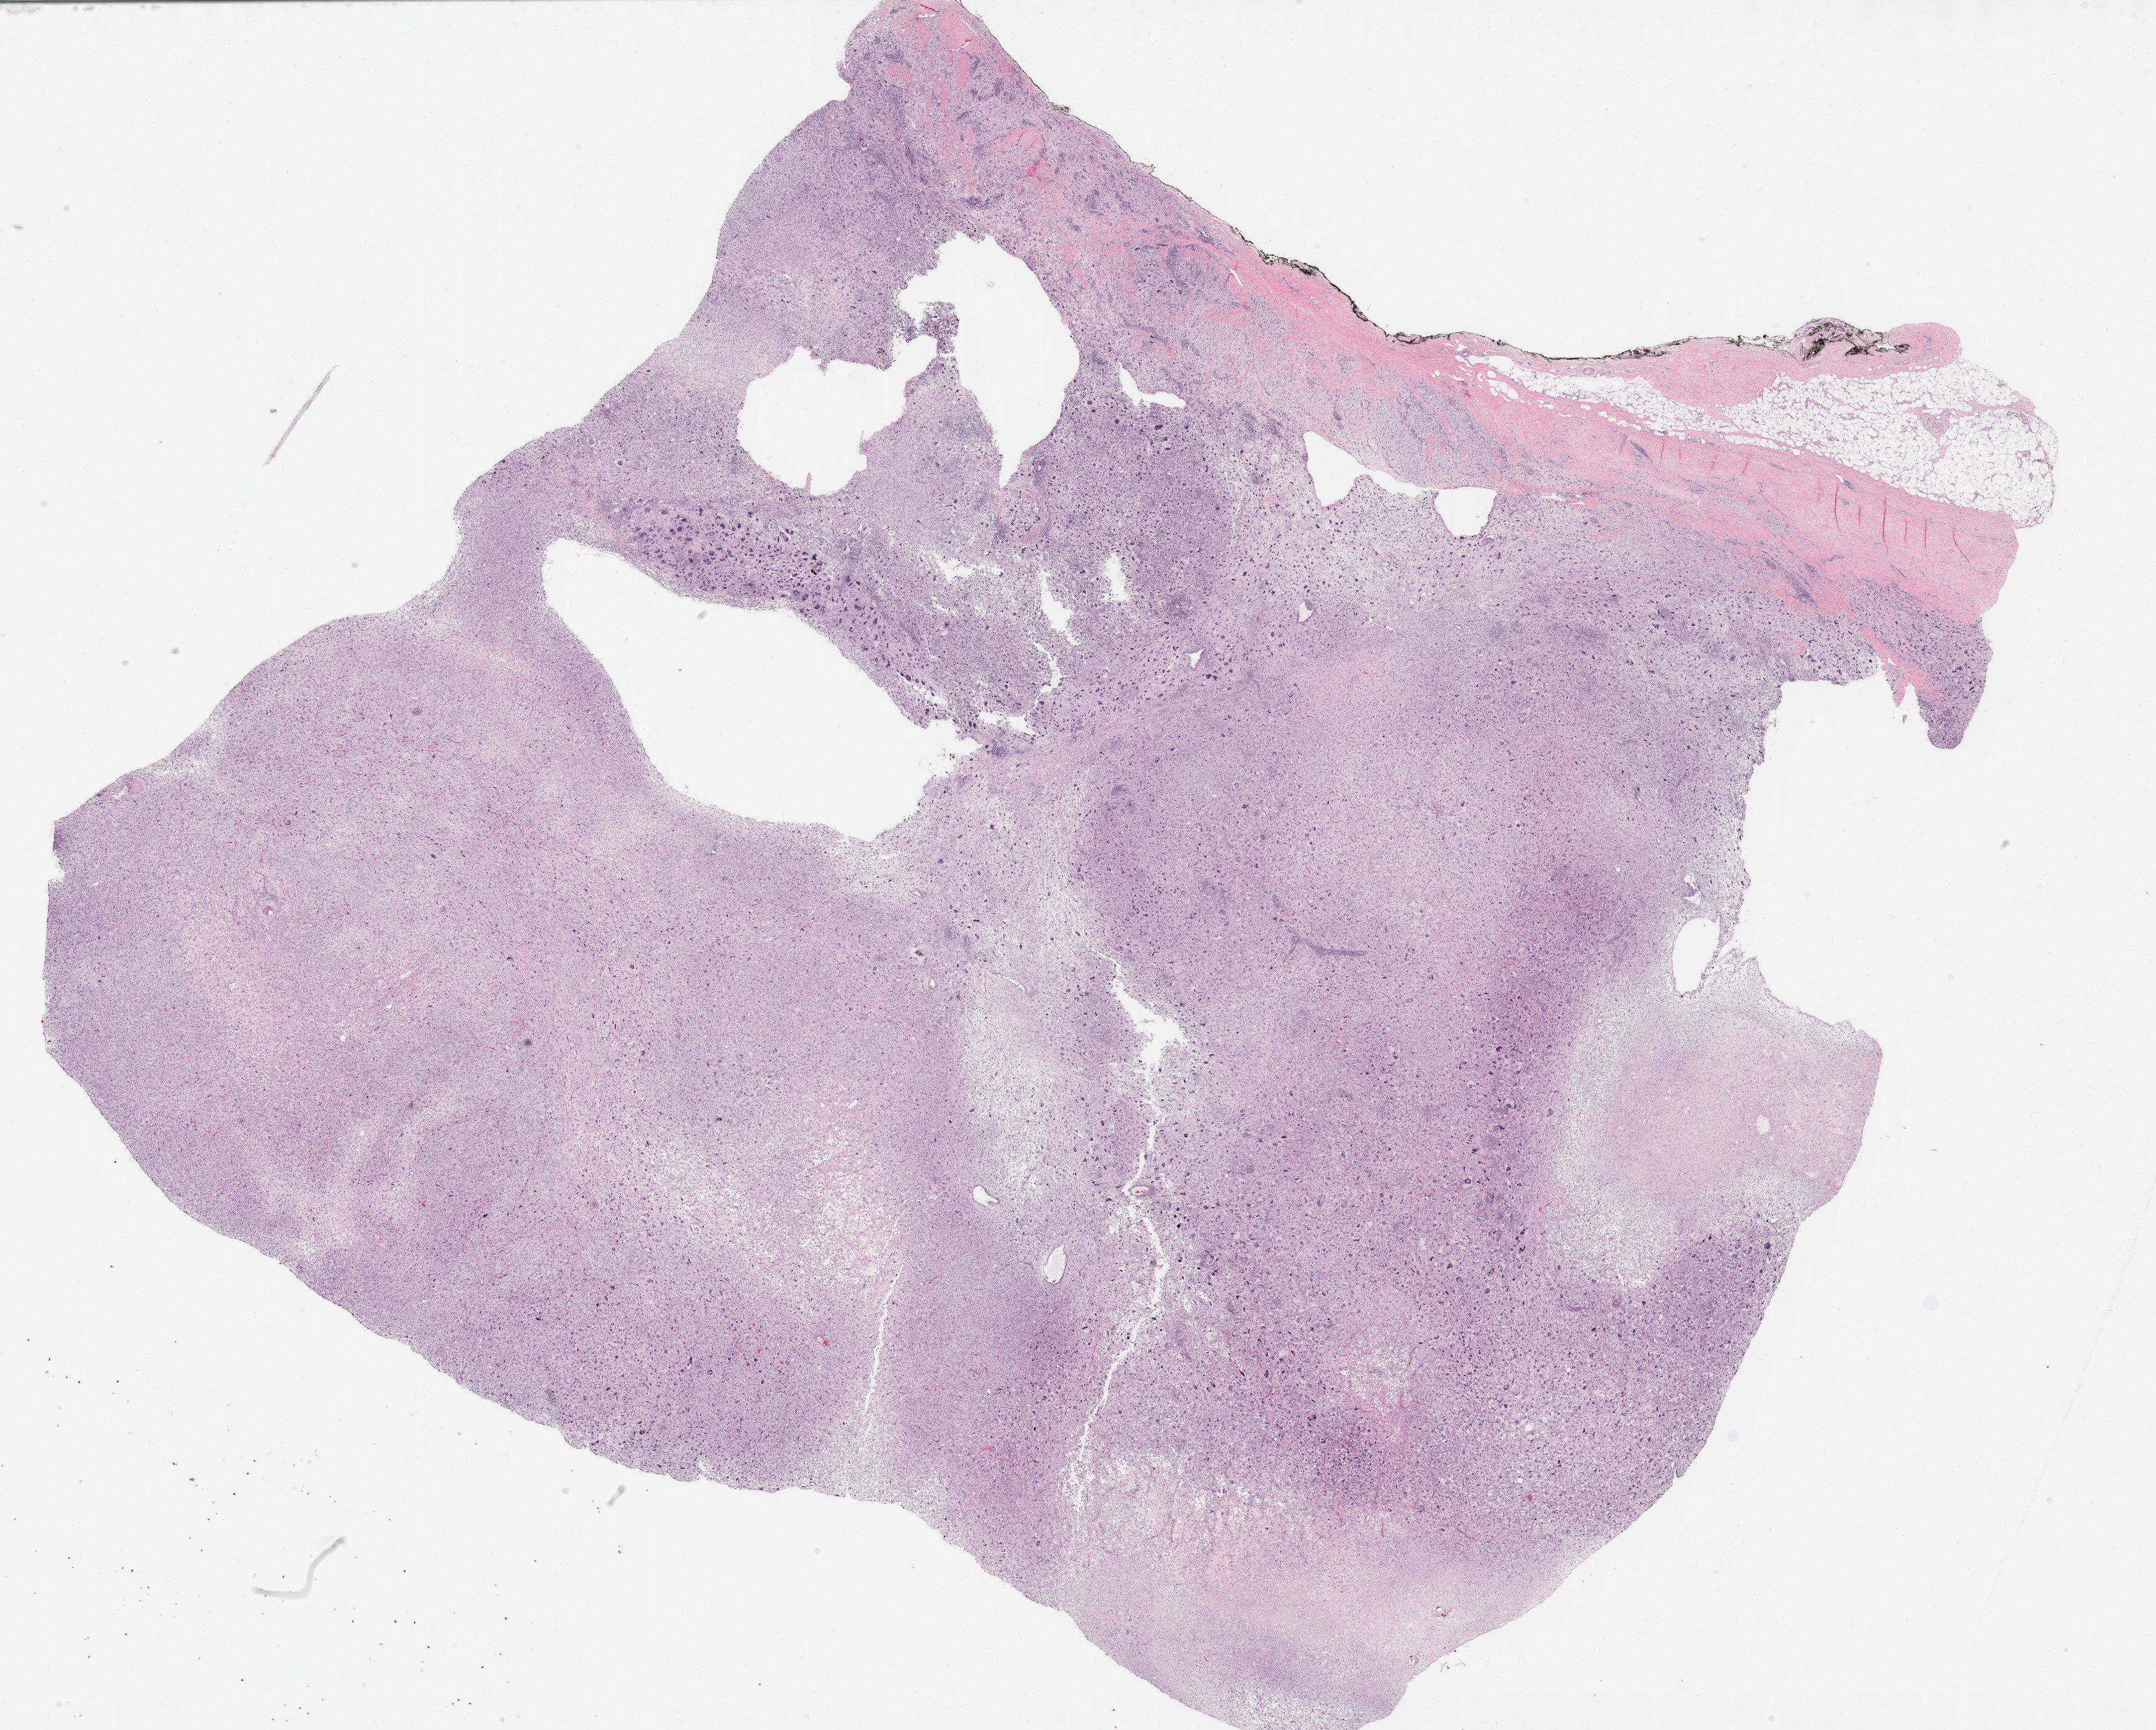
Digitized H&E-stained tissue section (whole slide) — a low-resolution overview of the entire scanned area, about 28.2 x 22.6 mm (from a 40x scan). Formalin-fixed paraffin-embedded (FFPE) diagnostic section. Sample: primary tumour, connective, subcutaneous and other soft tissues. Patient: female, age at initial diagnosis 67 years.
Pathologic diagnosis: Undifferentiated sarcoma (connective, subcutaneous and other soft tissues of lower limb and hip).